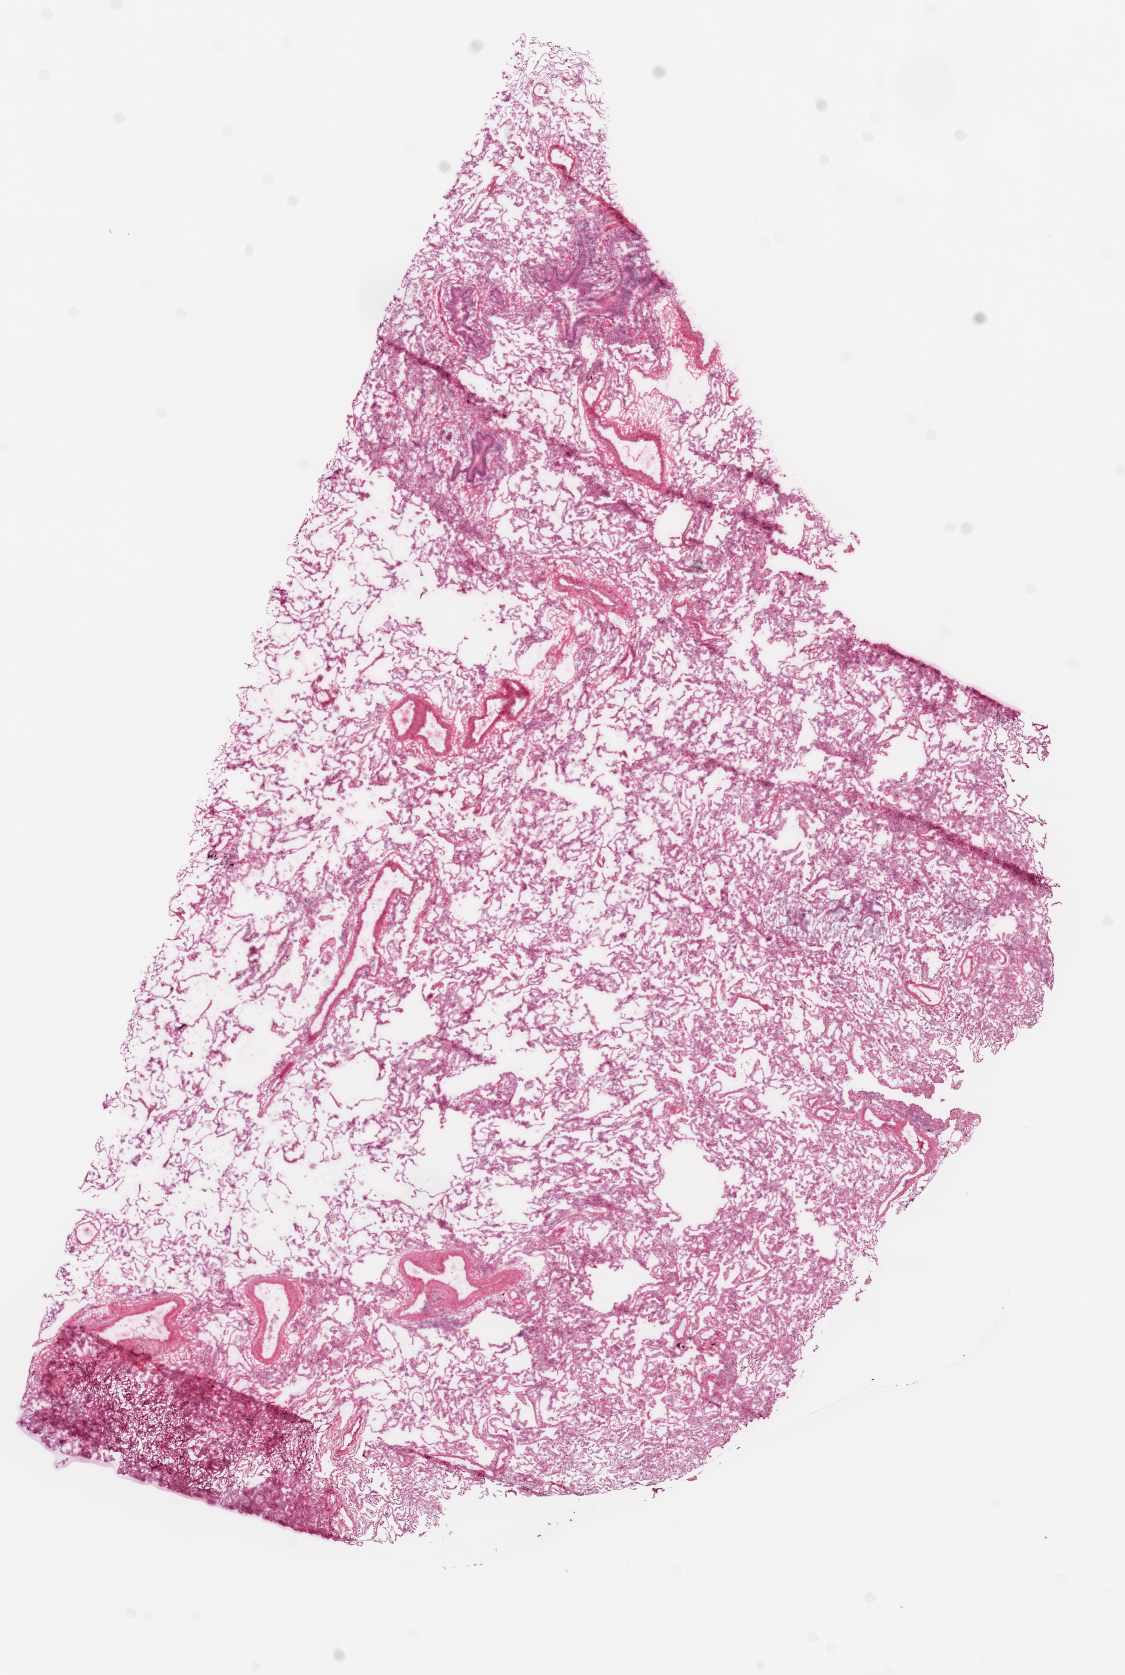
Whole-slide histology image, Hematoxylin and eosin (H&E) stained, a low-resolution overview of the entire scanned area, about 9.0 x 13.4 mm (from a 20x scan), frozen section, lung, solid tissue normal (non-tumour tissue) sample. Female patient; age at initial diagnosis 73 years.
This section: solid tissue normal (non-tumour) sample from the same patient. Patient diagnosis: Squamous cell carcinoma, NOS (overlapping lesion of lung).